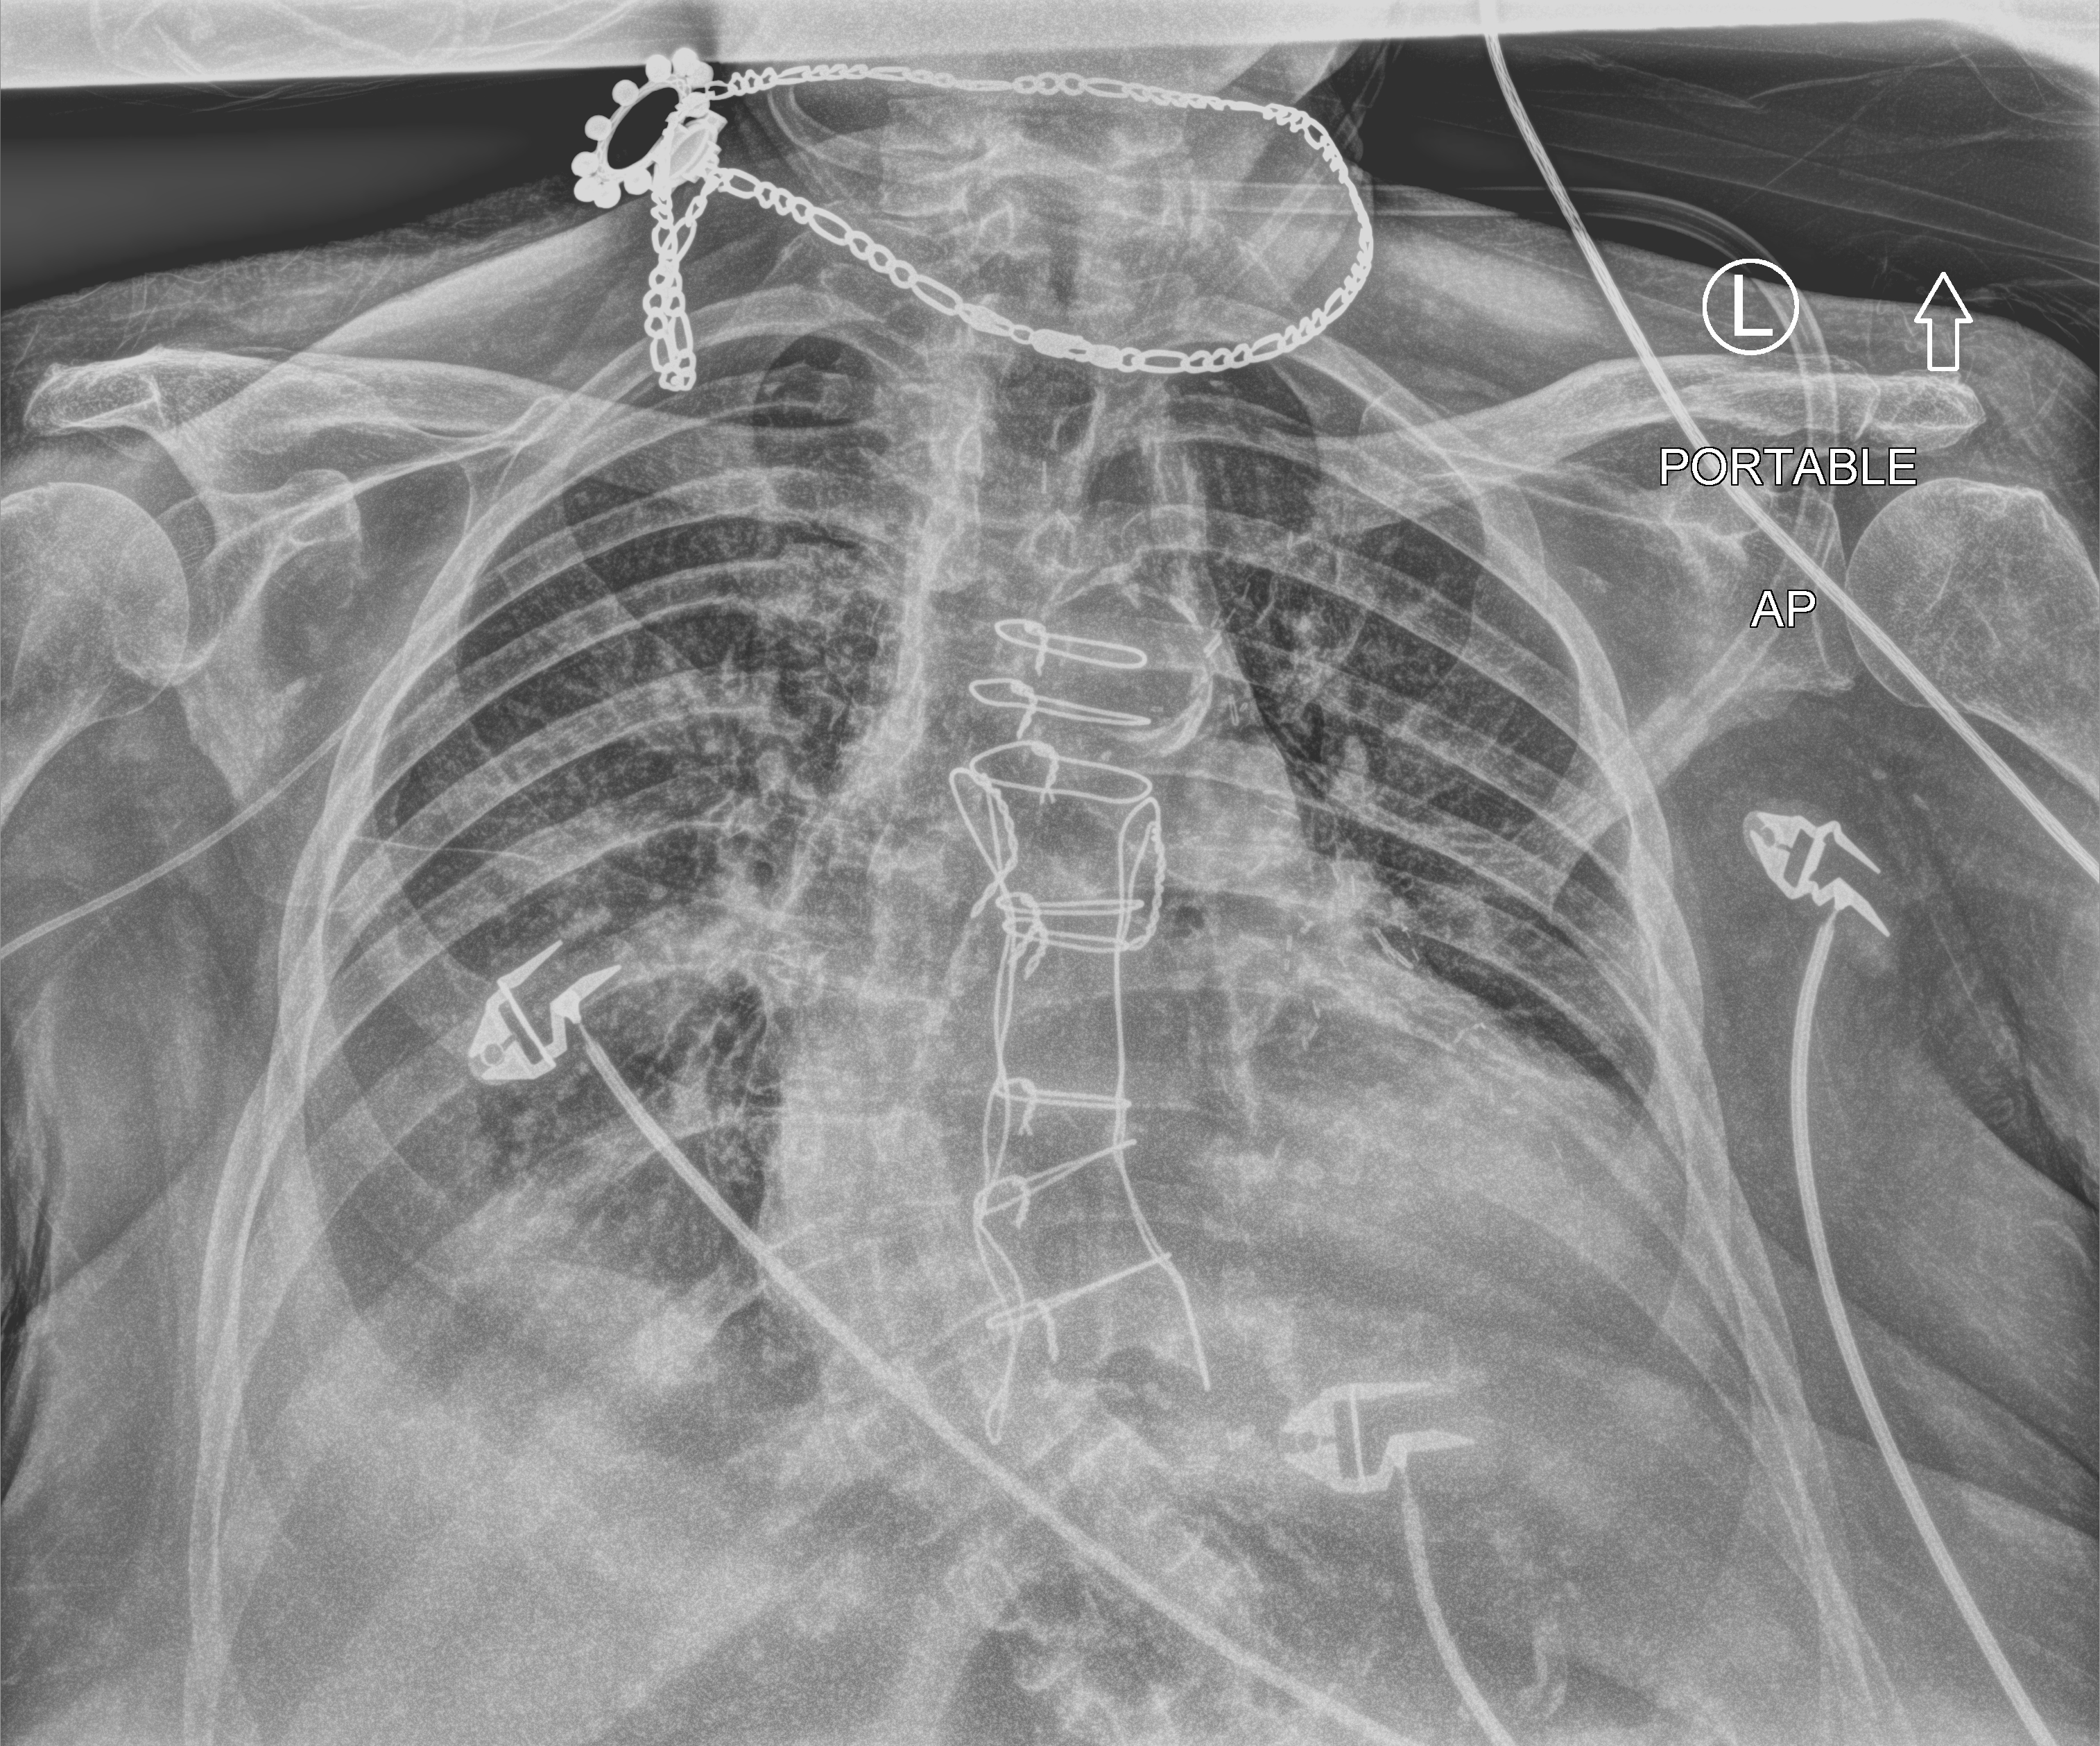
Chest X-ray (portable); anteroposterior (AP) projection. Female patient hospitalised with COVID-19, age 75–90 years.
Hospital-stay facts (about this admission, not read from this image; timing relative to this image not recorded): admitted to intensive care during this hospital stay: no.